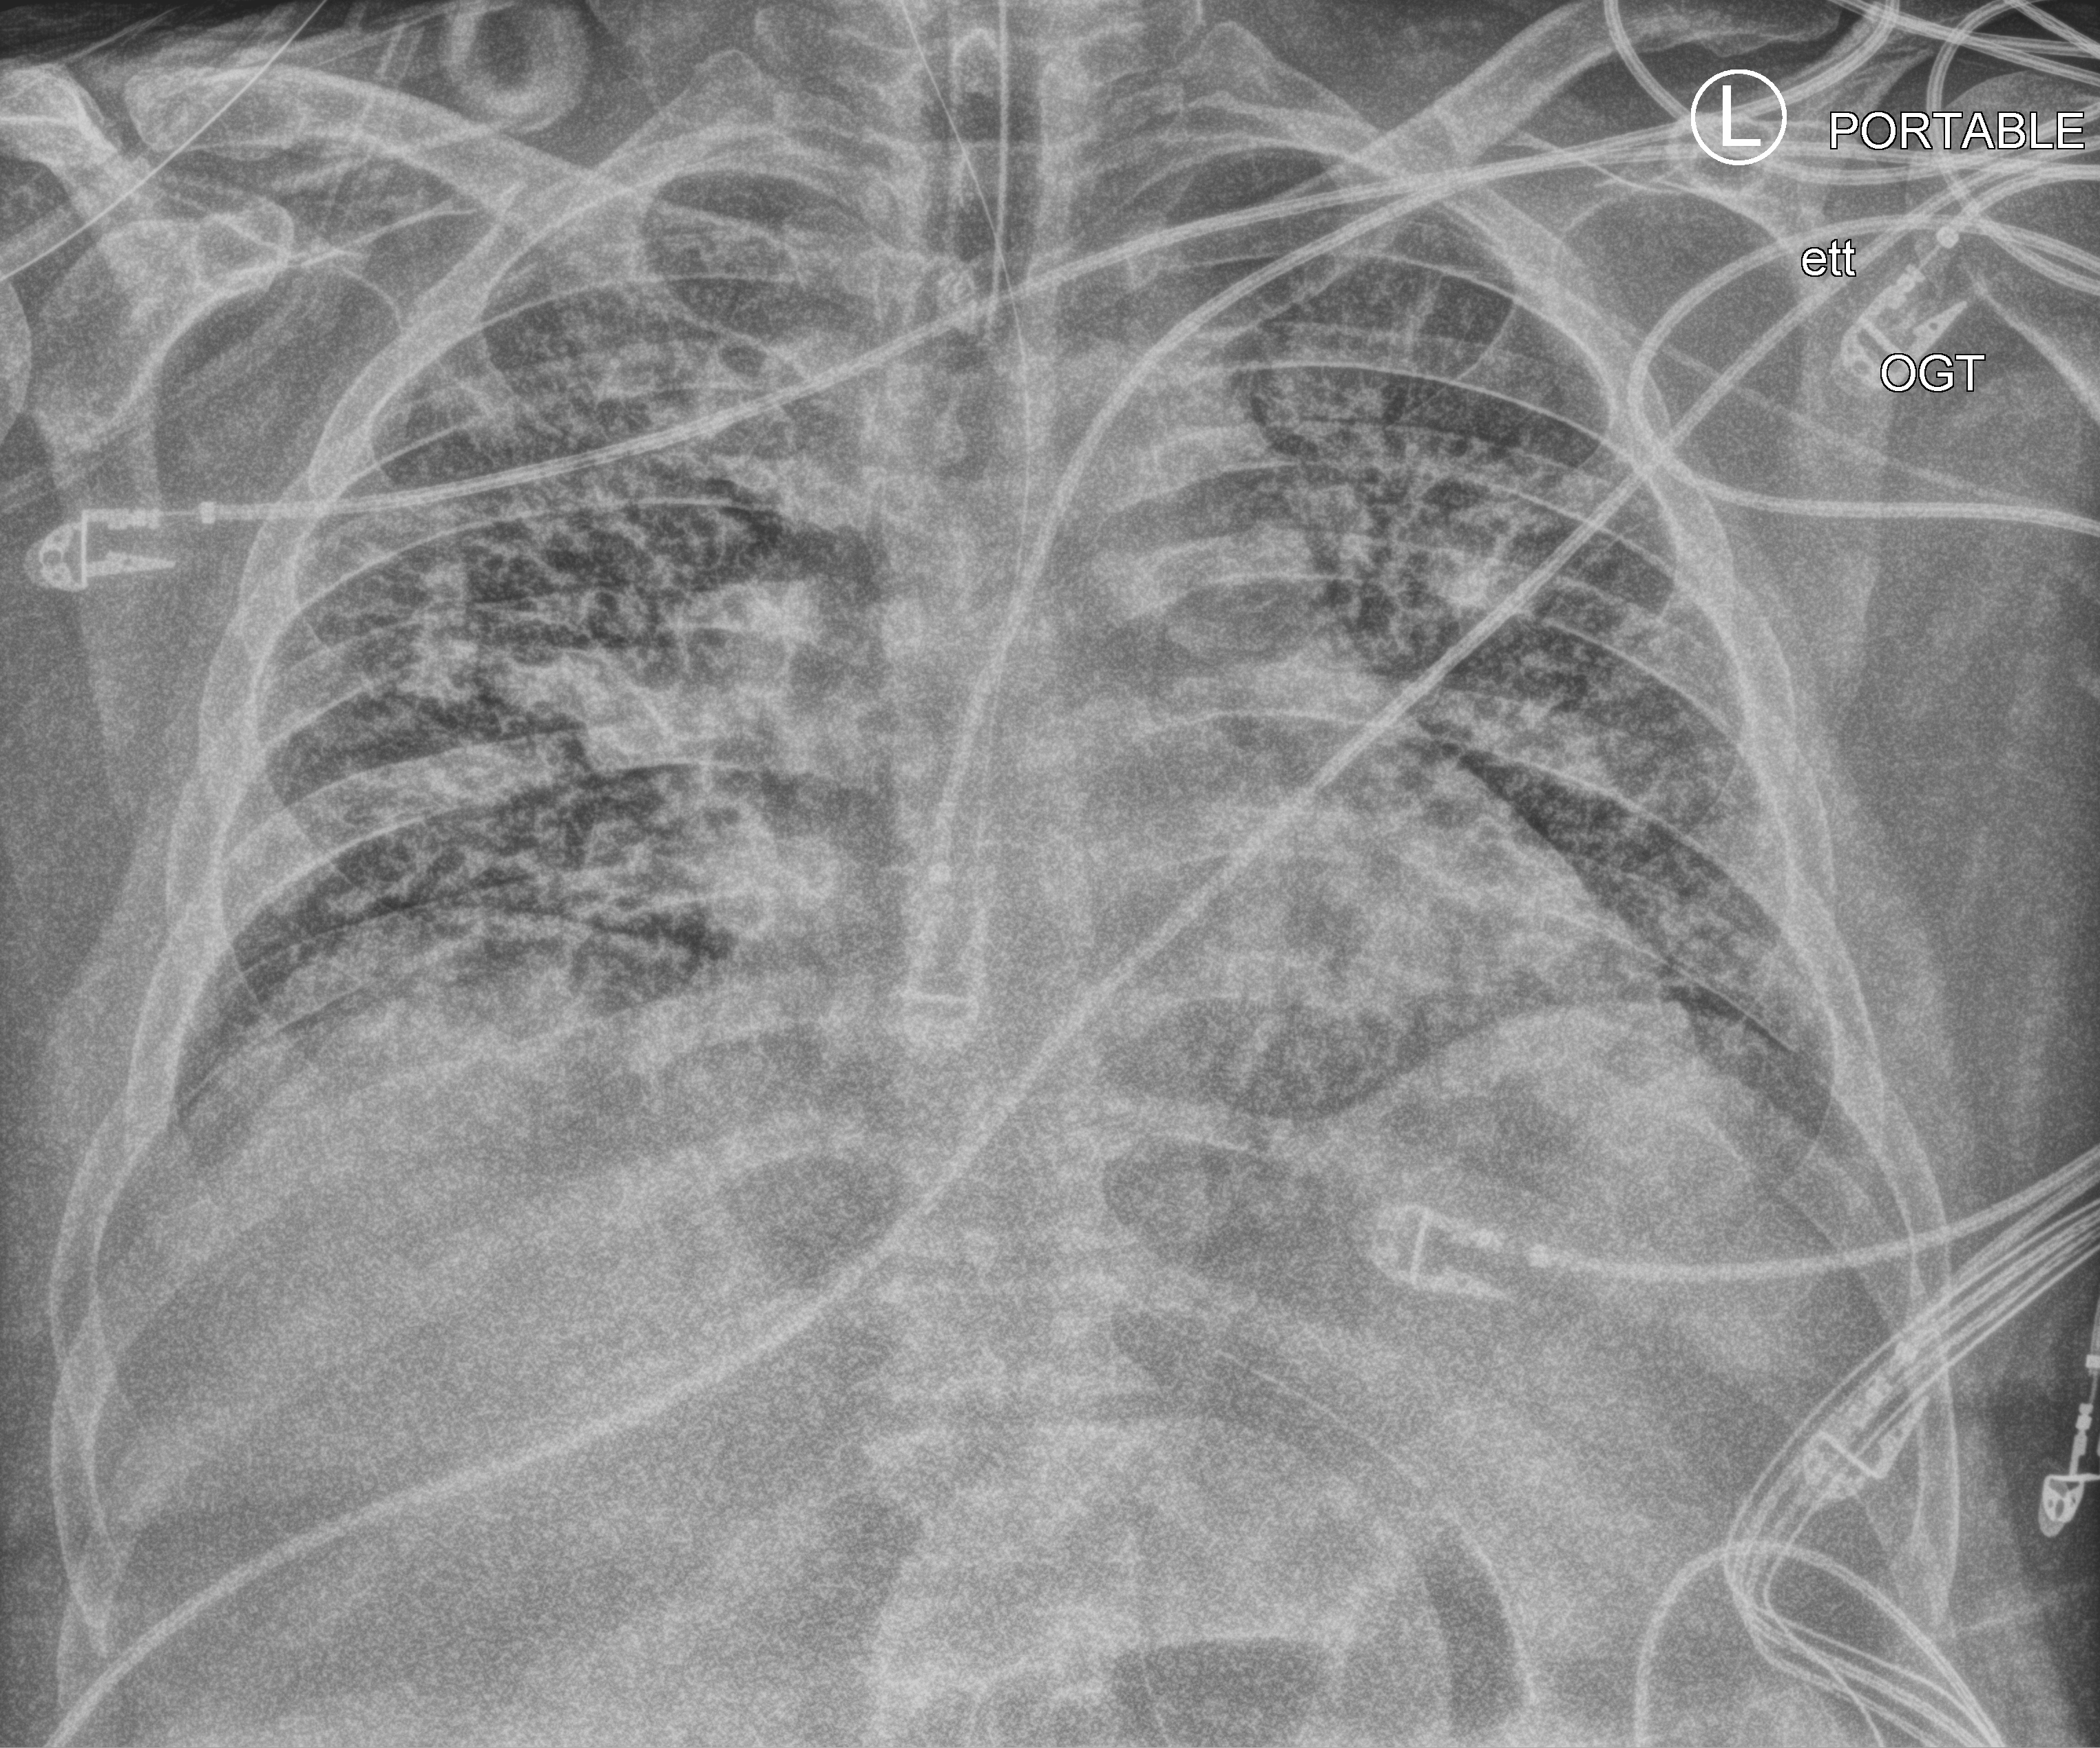
Bedside chest radiograph (computed radiography); anteroposterior (AP) projection. Patient hospitalised with COVID-19, aged 18–59 years.
Hospital-stay facts (about this admission, not read from this image; timing relative to this image not recorded): mechanically ventilated during this hospital stay: yes; length of hospital stay: 31 days.